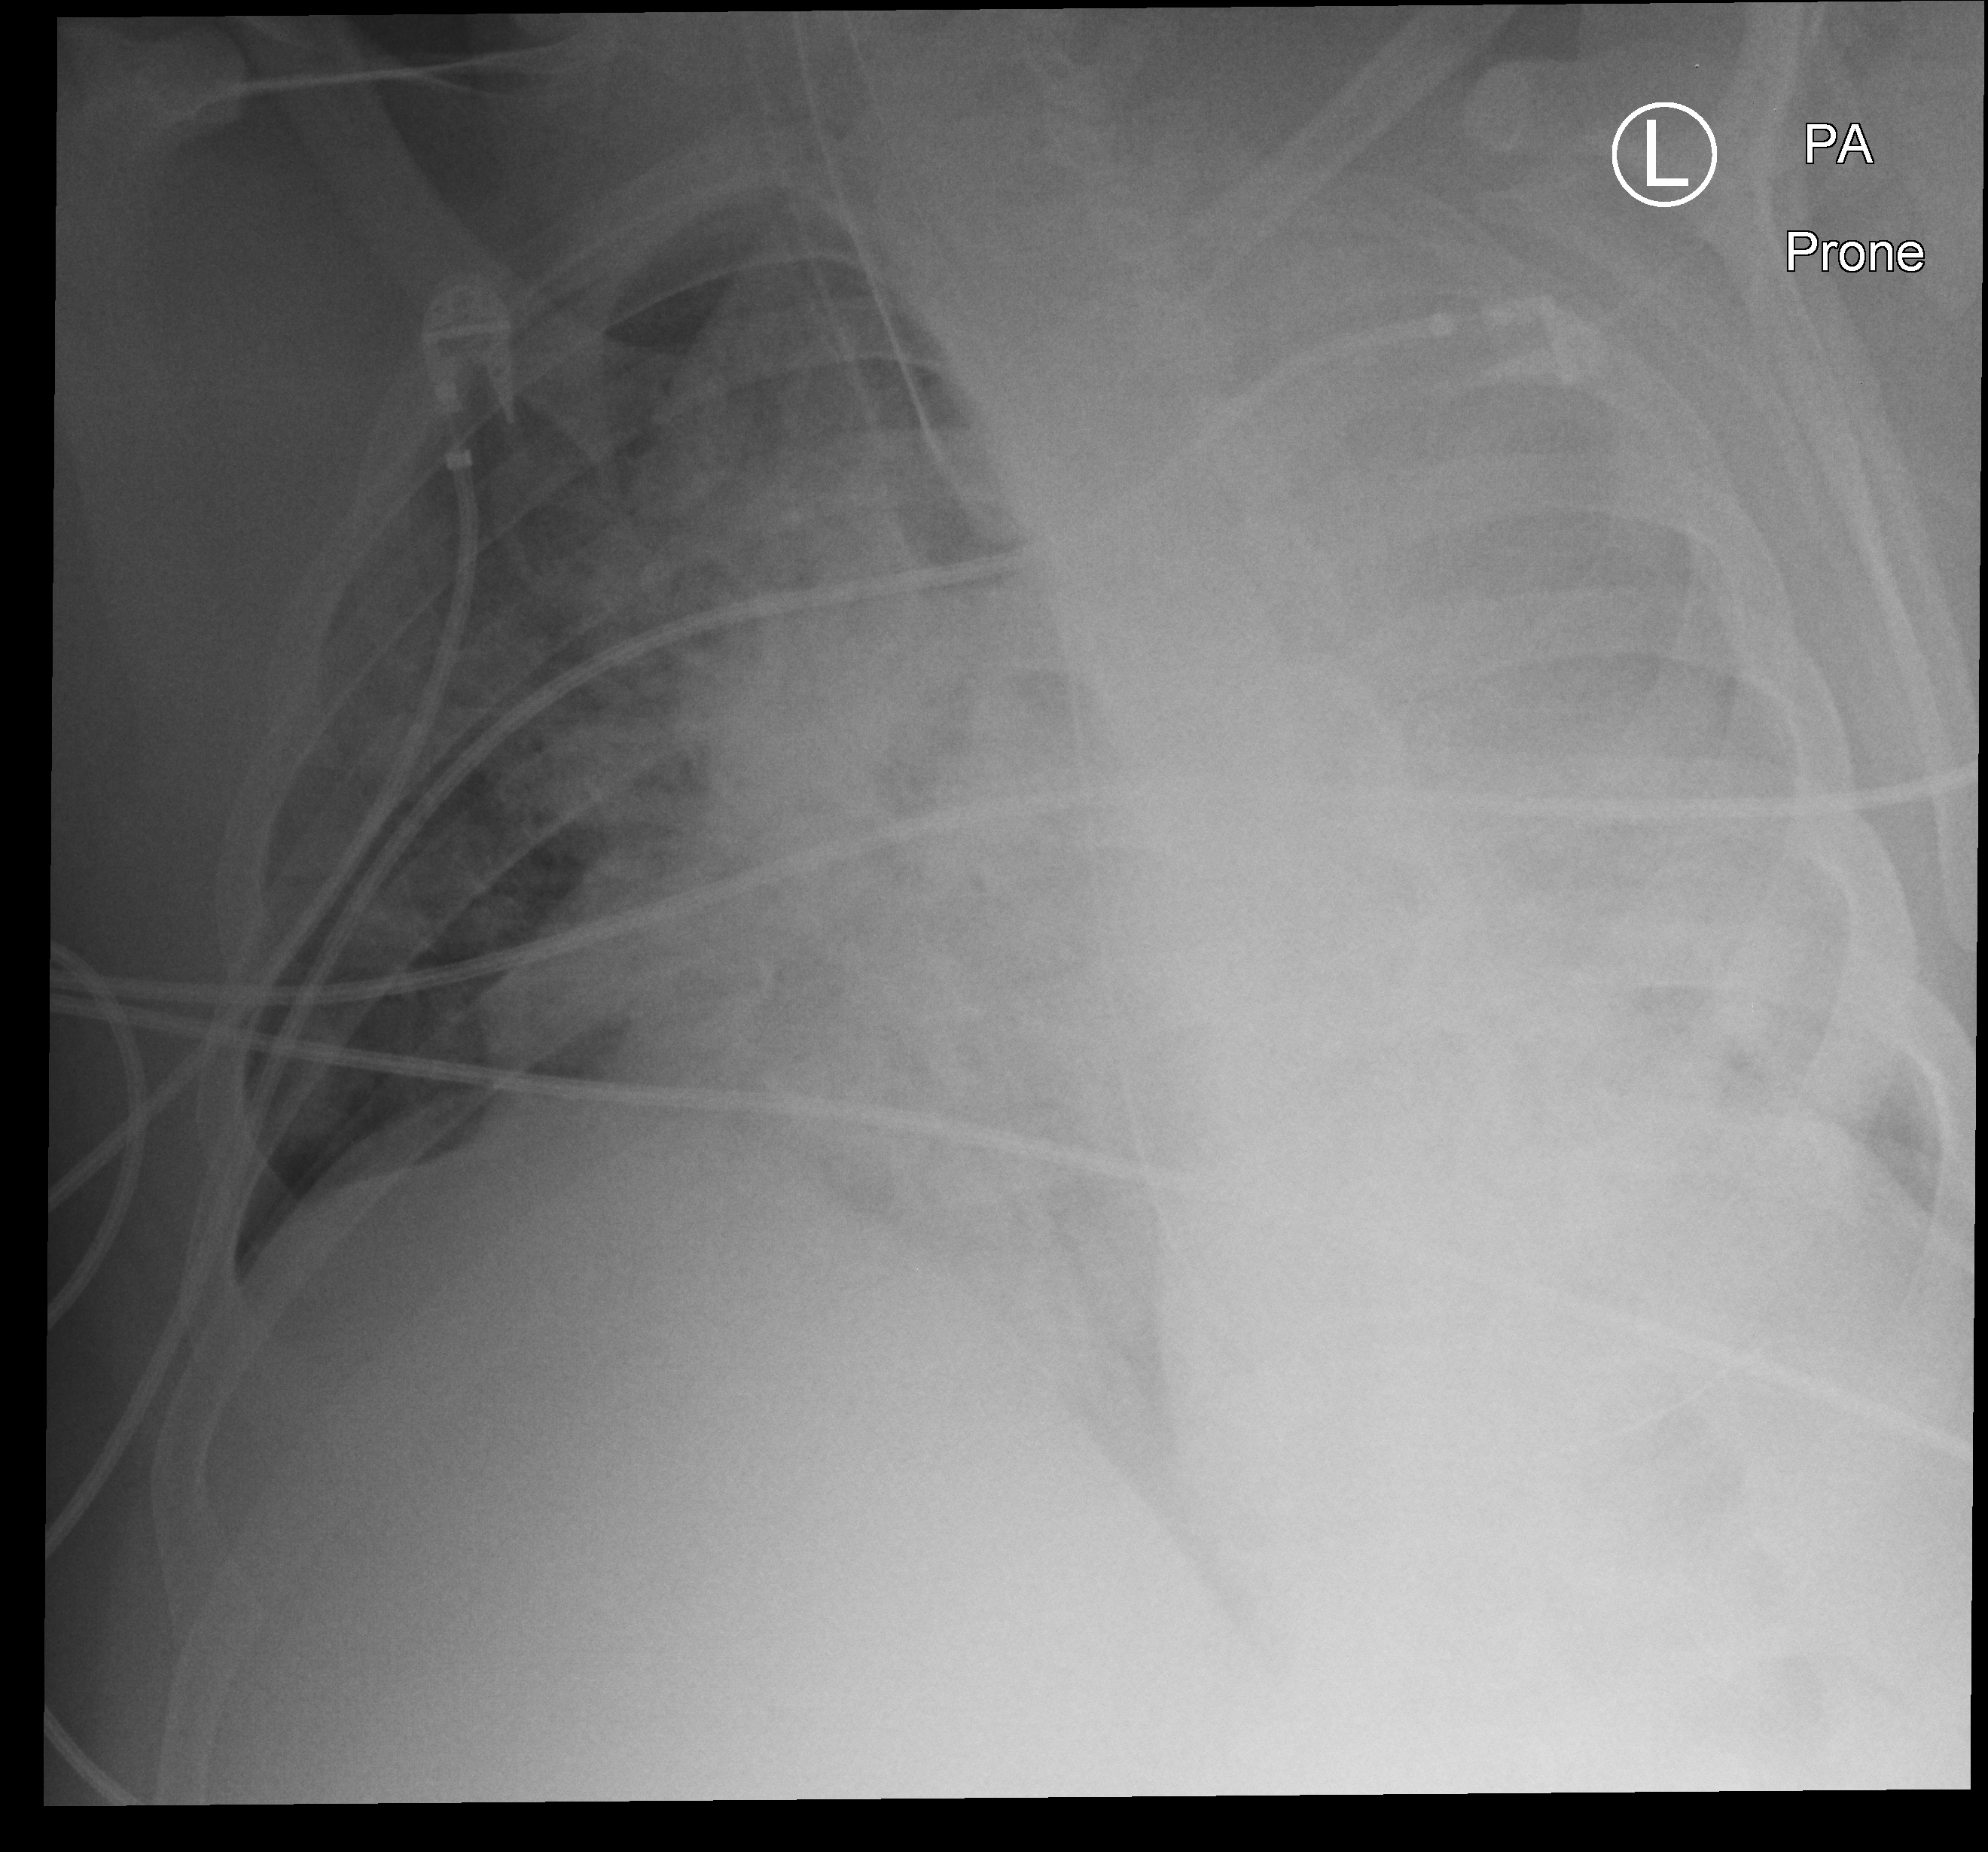
Bedside chest radiograph (computed radiography); posteroanterior (PA) projection. Patient hospitalised with COVID-19, aged 18–59 years.
From the hospital-stay record, not from the radiograph (when in the stay this image was taken is not recorded):
- admitted to intensive care during this hospital stay: yes
- chronic kidney disease (admission record): no